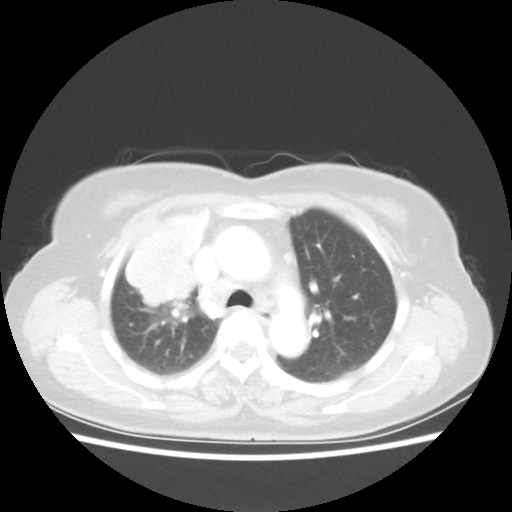
Chest CT, one axial slice; slice 37 of 55 in the series (ordered by position); lung window (W 1500 / L -600 HU); 512 × 512 image matrix, field of view 337 × 337 mm. Female patient, age 62 years. Case-level facts recorded for this patient, not image findings: clinical TNM (as recorded): T4 N3 M0.
Annotated regions visible in this slice (bounding box drawn by a radiologist):
- lung tumour (recorded histology: squamous cell carcinoma): bounding box (x1, y1, x2, y2) in pixels: (121, 202, 213, 315)